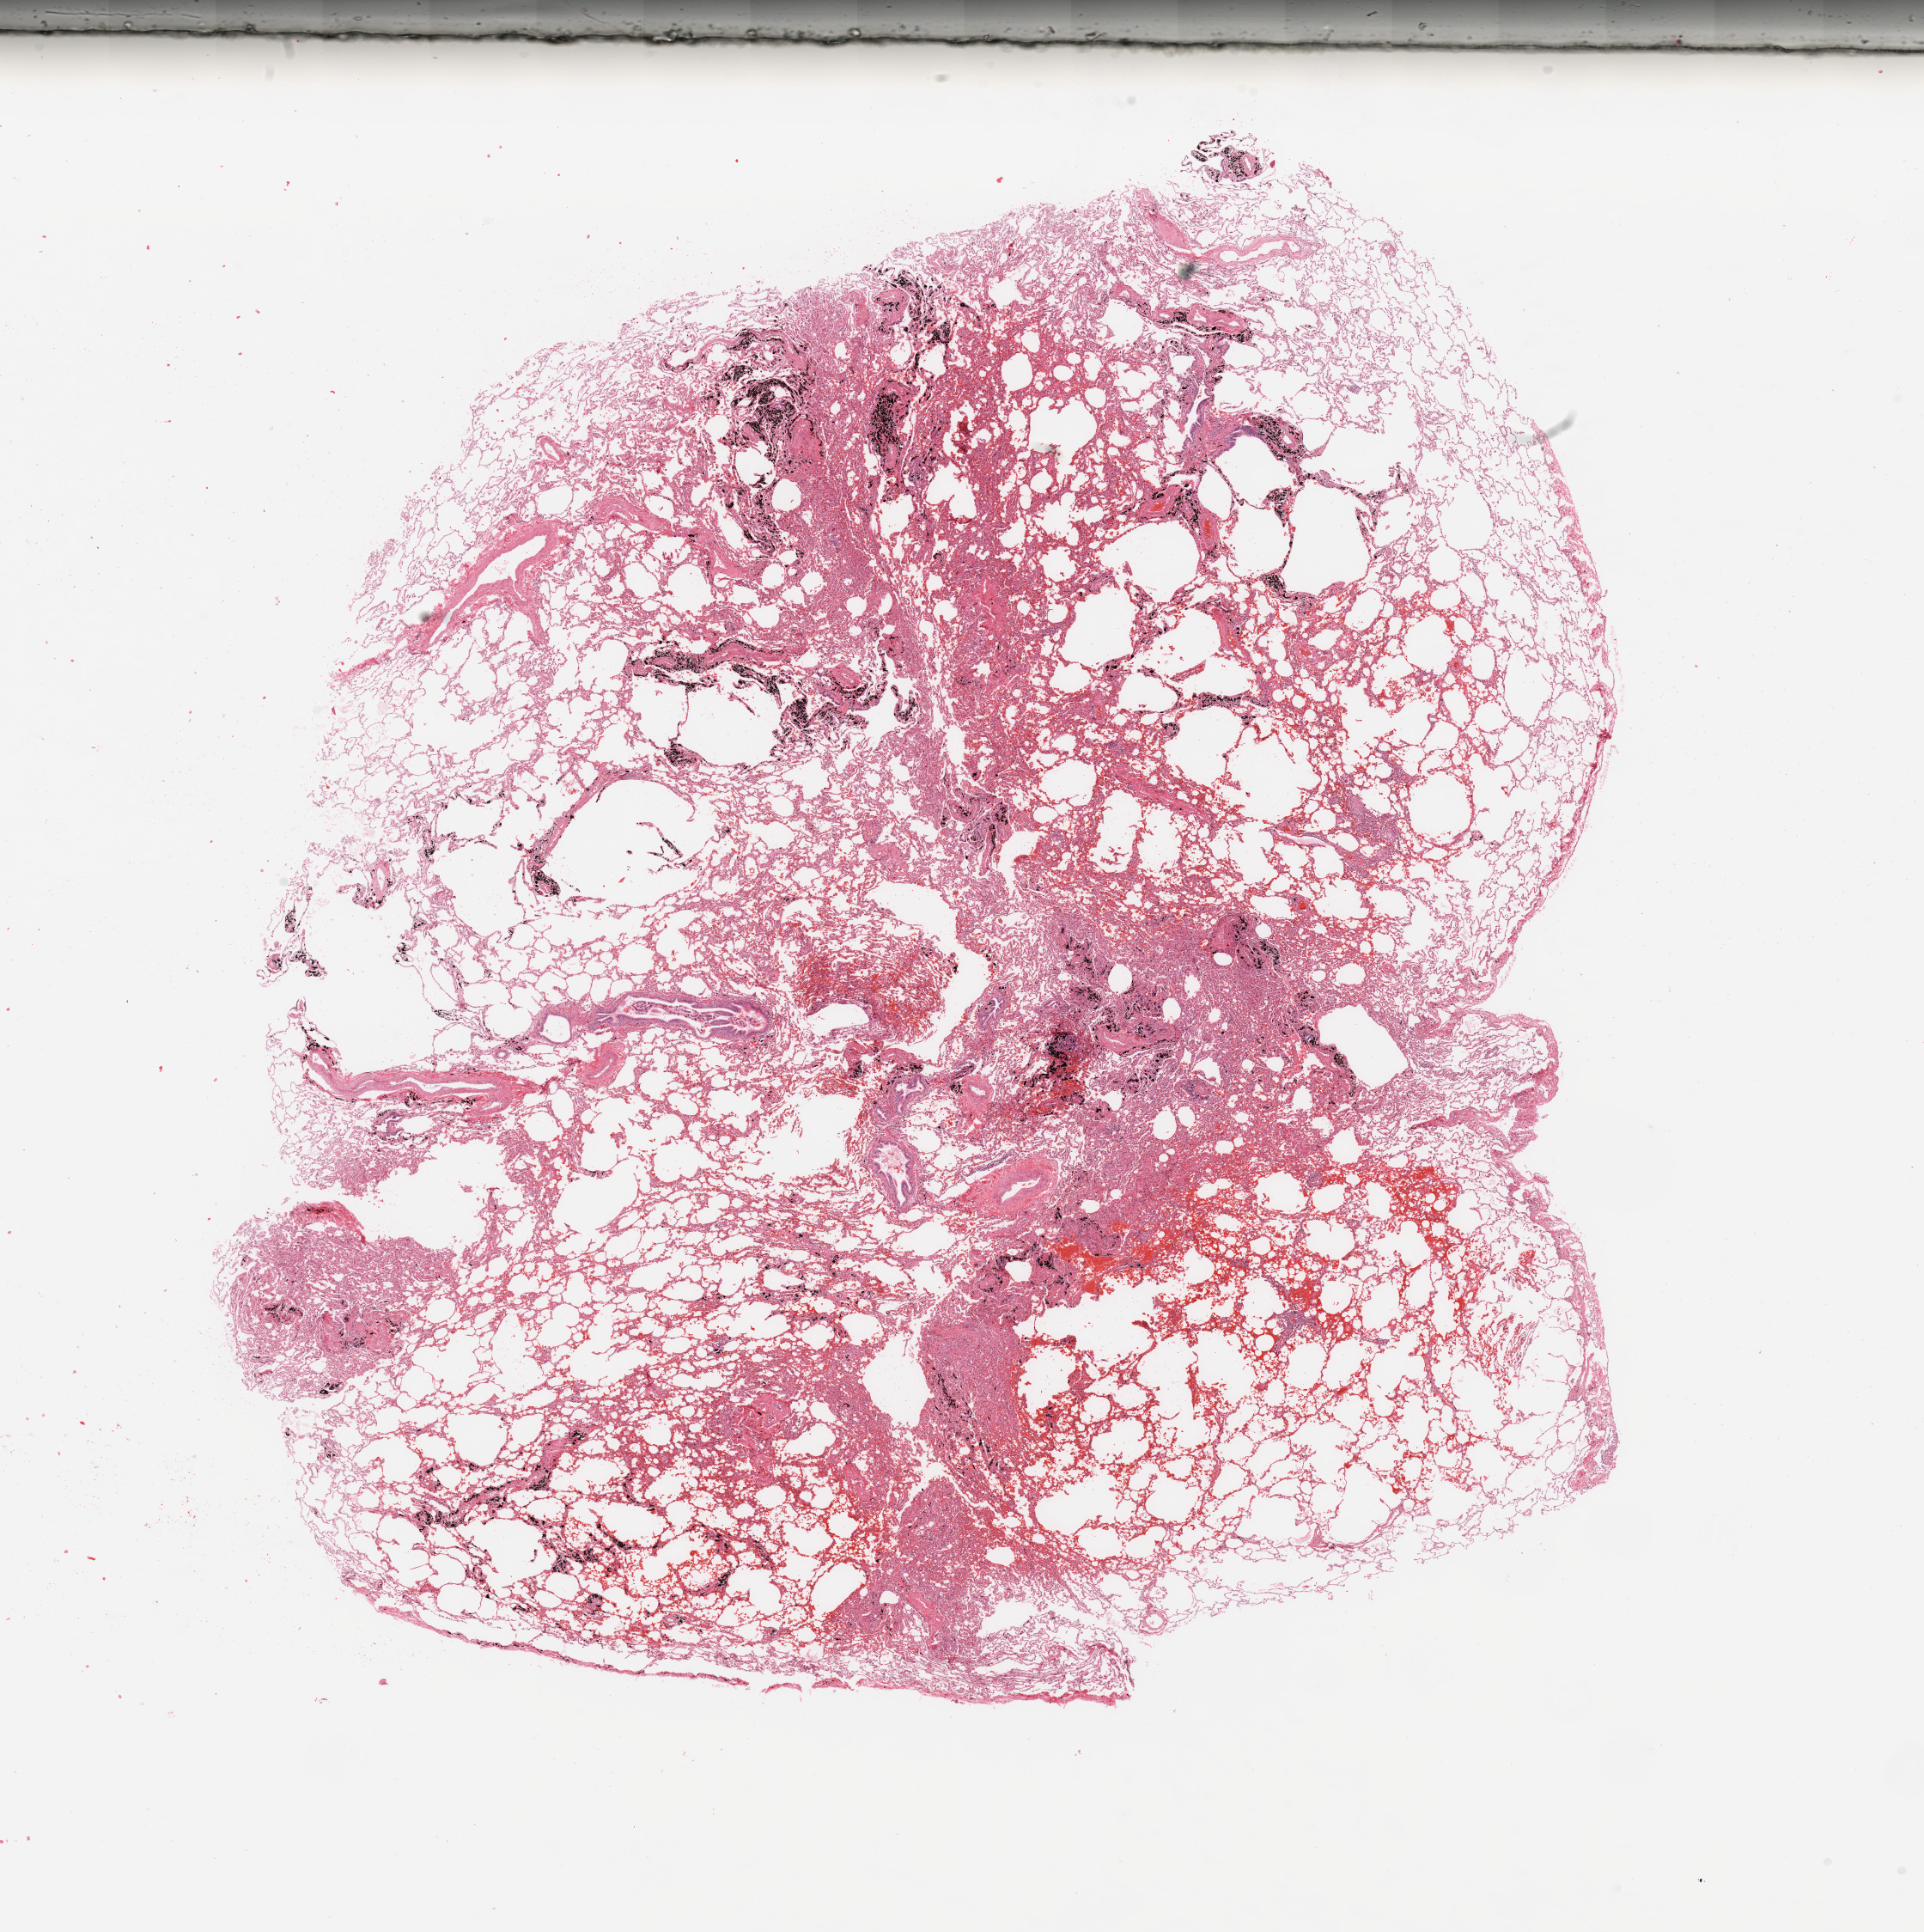
Hematoxylin and eosin (H&E) stained whole-slide image — a low-resolution overview of the entire scanned area, about 17.7 x 17.8 mm (acquisition: 20x scan). Normal (non-tumour) tissue sample, lung. 54-year-old male patient.
- this section: normal (non-tumour) tissue from the same patient
- patient diagnosis: Adenocarcinoma, NOS